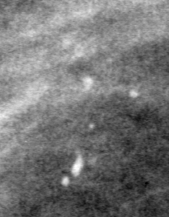
Crop from a digitized film mammogram around one marked abnormality; left breast; MLO view; BI-RADS breast density category 2 (scale 1–4).
- Calcifications, morphology pleomorphic, distribution clustered; BI-RADS assessment category 4; pathology result (as recorded, not read from the image): benign.